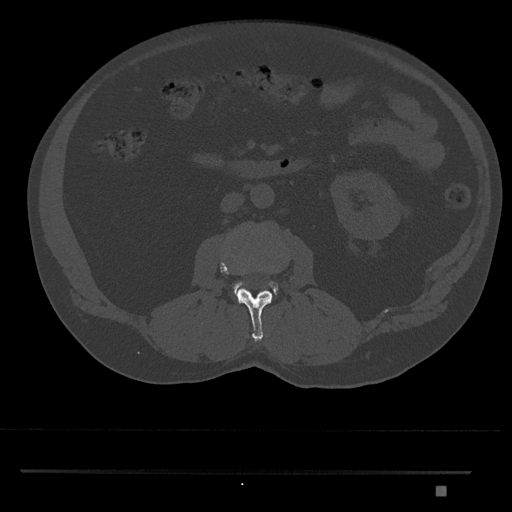
CT including the spine, one axial slice. Slice 726 of 1134 in the series (ordered by position). Reconstruction kernel Br40s/3. 120 kVp. Bone window (W 1800 / L 400 HU). 512 × 512 image matrix, field of view 429 × 429 mm. Male patient, age 65 years. Case-level facts recorded for this patient, not image findings: primary cancer: prostate.
Annotated regions visible in this slice (semi-automatic segmentation, software-assisted and operator-edited):
- L2 vertebra: bounding box <220,261,272,342> (left, top, right, bottom; pixels)
- L3 vertebra: <233,281,278,294>